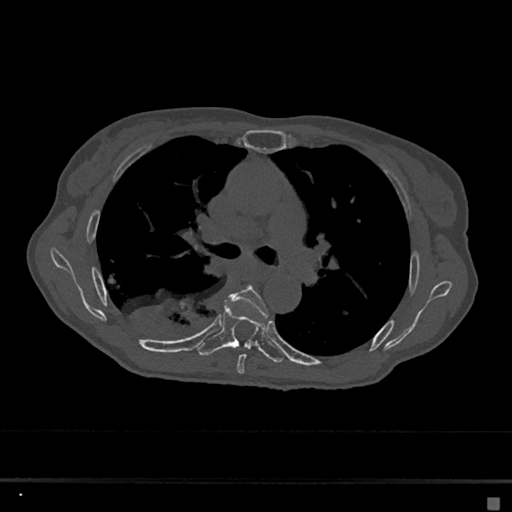
CT including the spine, one axial slice. Position 436 of 797 along the scan axis. Reconstruction kernel Br40s/3. 120 kVp. Bone window (W 1800 / L 400 HU). 0.5 mm slice thickness. 512 × 512 image matrix. Patient: female, 68 years. From the clinical record (not read from this slice): primary cancer: renal.
Outlined on this slice (semi-automatically segmented with operator editing):
- T5 vertebra: box from (x=227, y=285) to (x=268, y=374) px
- T6 vertebra: (x=197, y=300)–(x=284, y=363)